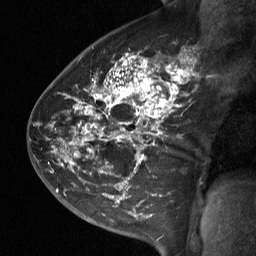
Breast MRI (dynamic contrast-enhanced), one sagittal slice. Position 42 of 64 along the scan axis. Dynamic contrast-enhanced study with each time point stored as its own series, time point 2 of 3 at this slice position (early post-contrast, ordered by acquisition time). 1.5 T. TE 4.8 ms, TR 27 ms. 2 mm slice thickness. 256 × 256 image matrix. Female patient, age 42 years. From the clinical record (not read from this slice): setting: breast cancer imaged before/during neoadjuvant chemotherapy; receptor status: triple-negative.
Structures marked on this image (semi-automatic segmentation, software-assisted and operator-edited):
- analysis volume of interest (the breast-tissue region the enhancement analysis was run in; not a lesion): bounding box [x1, y1, x2, y2] px = [49, 45, 192, 197]
- tumour enhancement mask (voxels above the 90 % enhancement threshold inside the analysis volume of interest): [57, 55, 189, 191]